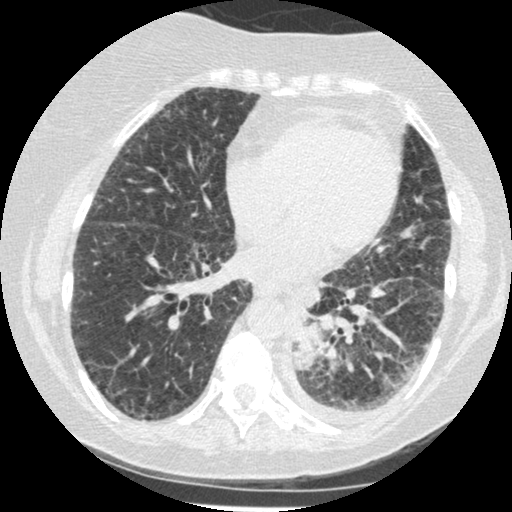
Axial slice from a low-dose chest CT screening exam; third screening round (two years after baseline); lung window (W 1500 / L -600 HU); 1.25 mm slice thickness; standard (soft-tissue) reconstruction kernel (STANDARD); 120 kVp; slice 261 of 341 in the series; 512 × 512 image matrix, field of view 310 × 310 mm. Female participant, aged 60 years at enrolment. Former smoker at enrolment.
Lesion marked by an expert reader, box from (x=279, y=301) to (x=344, y=377) px. The exam's reader record, not a measurement of the box and not confirmed to be the same lesion: non-calcified nodule or mass ≥4 mm, left lower lobe, 54 × 38 mm, smooth margins, soft tissue attenuation, pre-existing on the prior screen: yes; interval growth: yes.